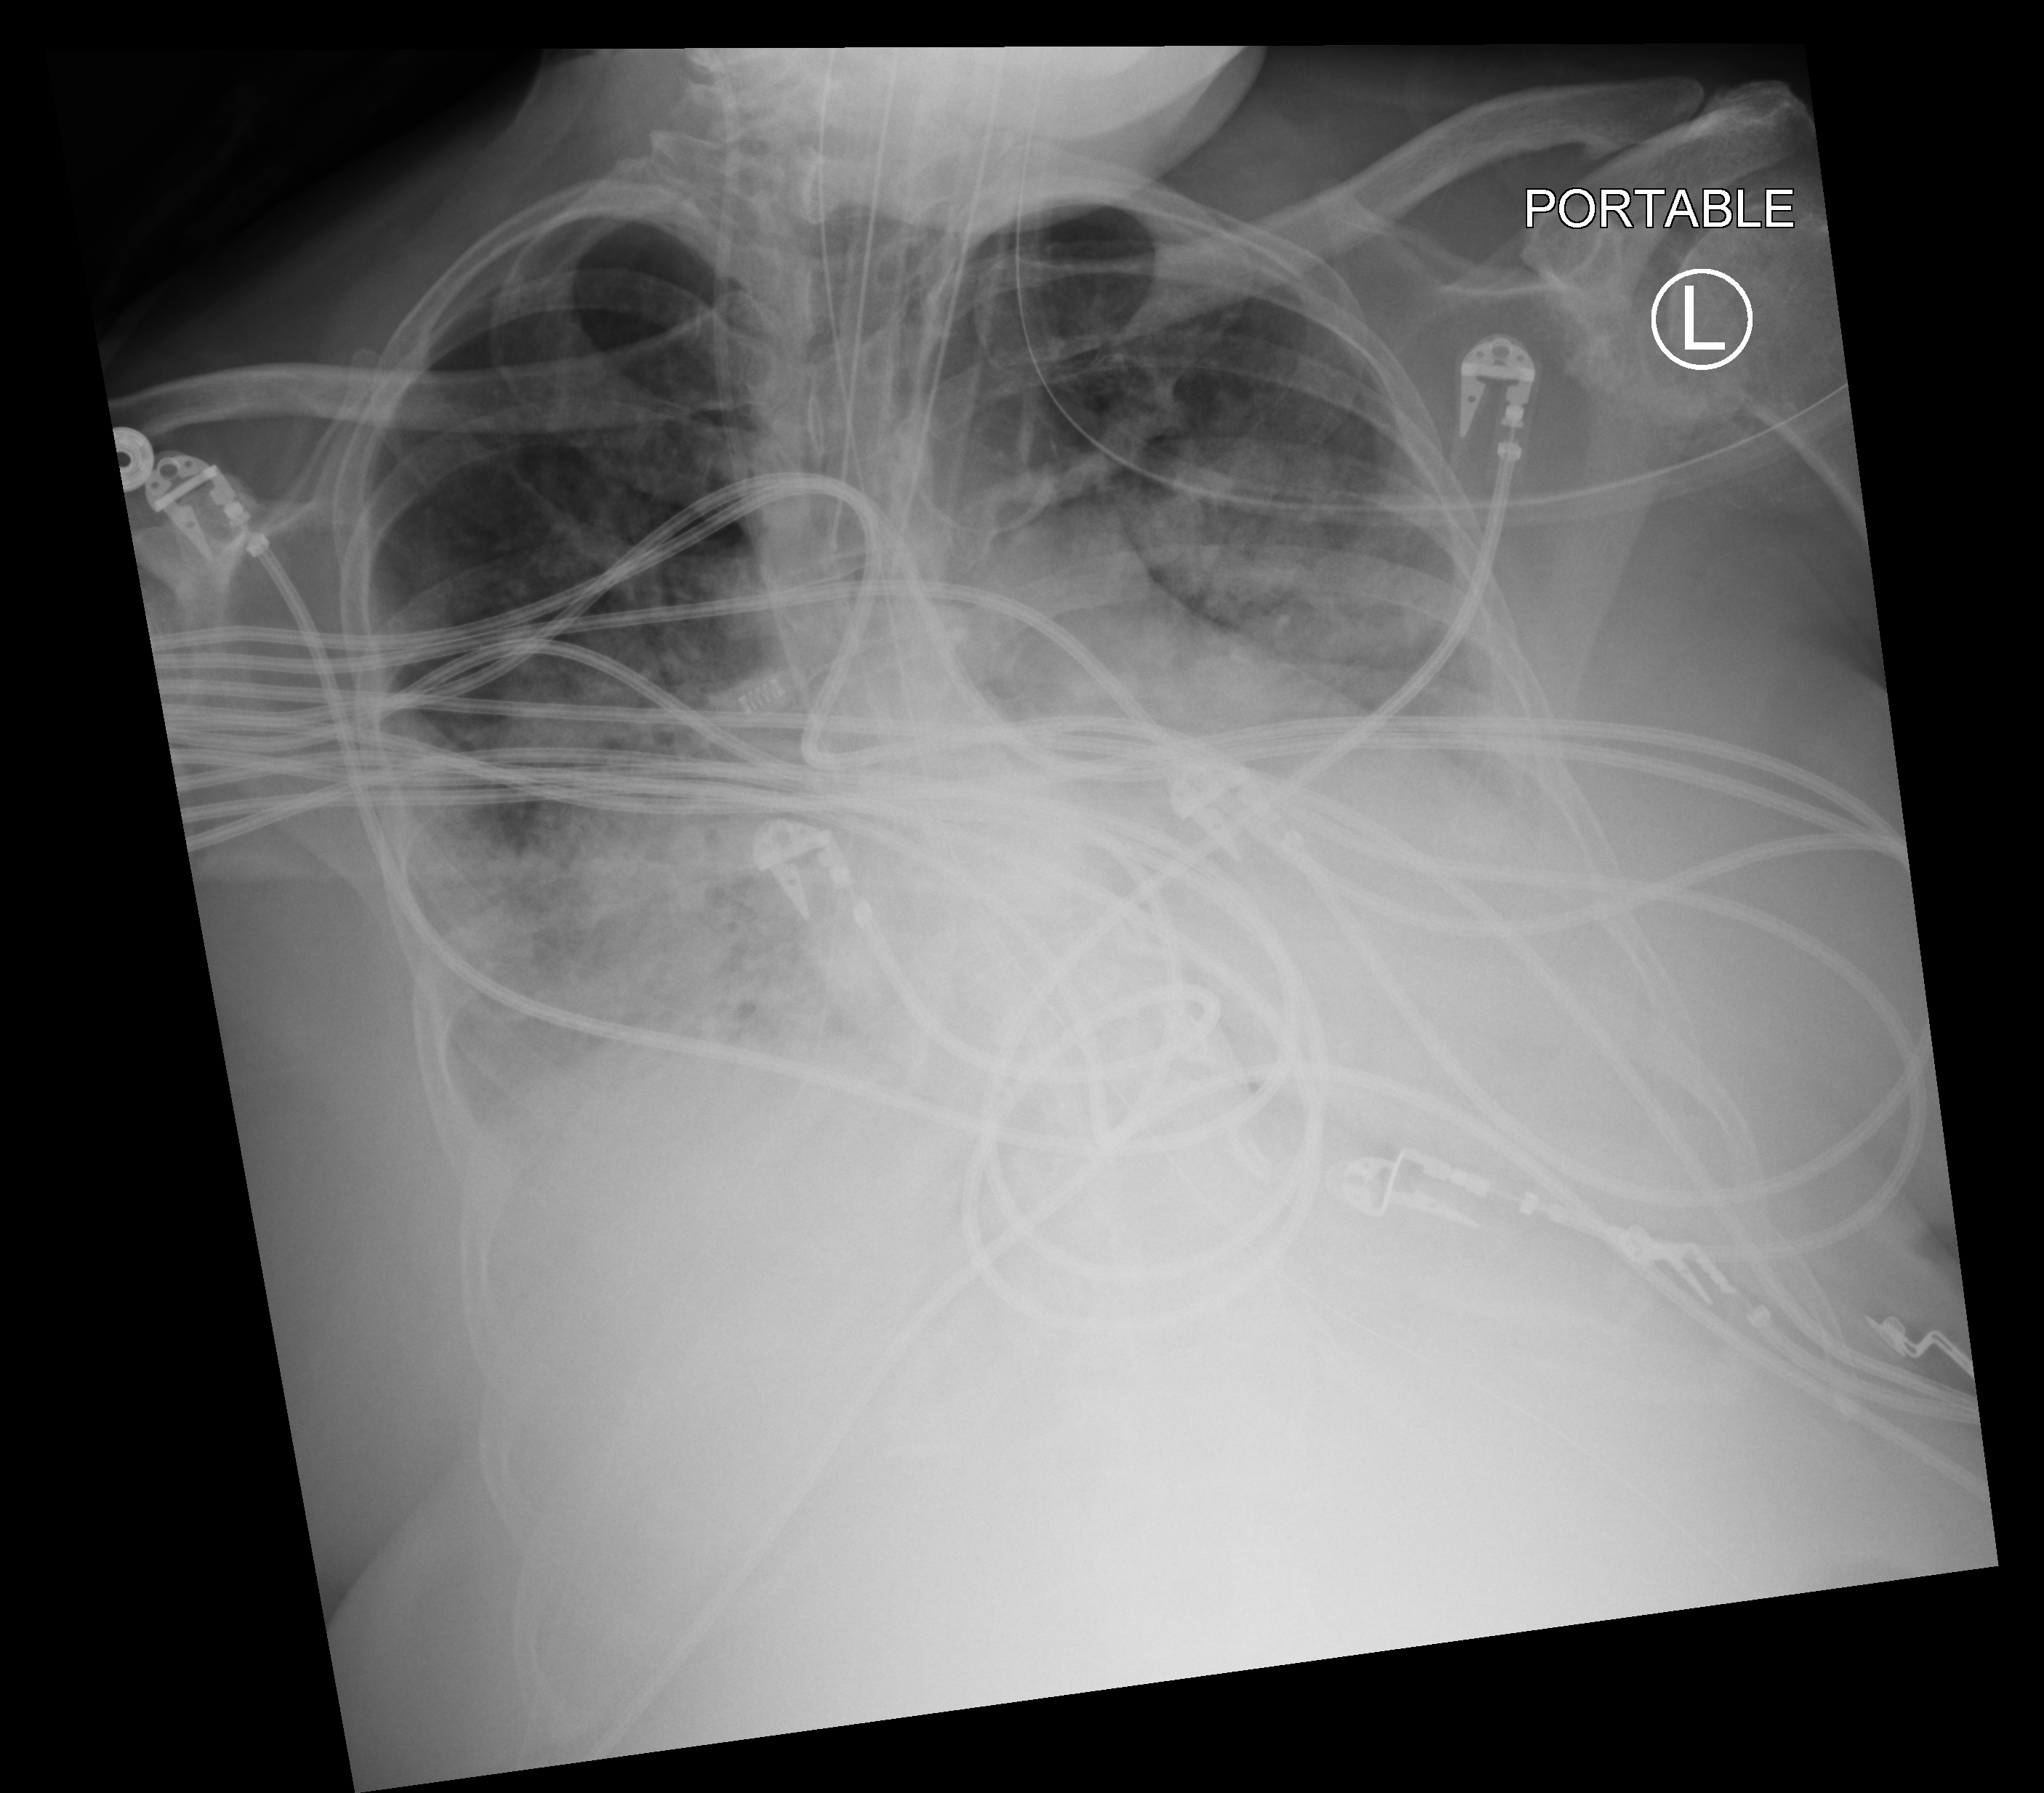
Bedside chest radiograph (computed radiography); anteroposterior (AP) projection. Female patient hospitalised with COVID-19, age 60–74 years.
Admission-level facts for this patient (not findings on this image; timing relative to this image not recorded): admitted to intensive care during this hospital stay: yes; mechanically ventilated during this hospital stay: yes.